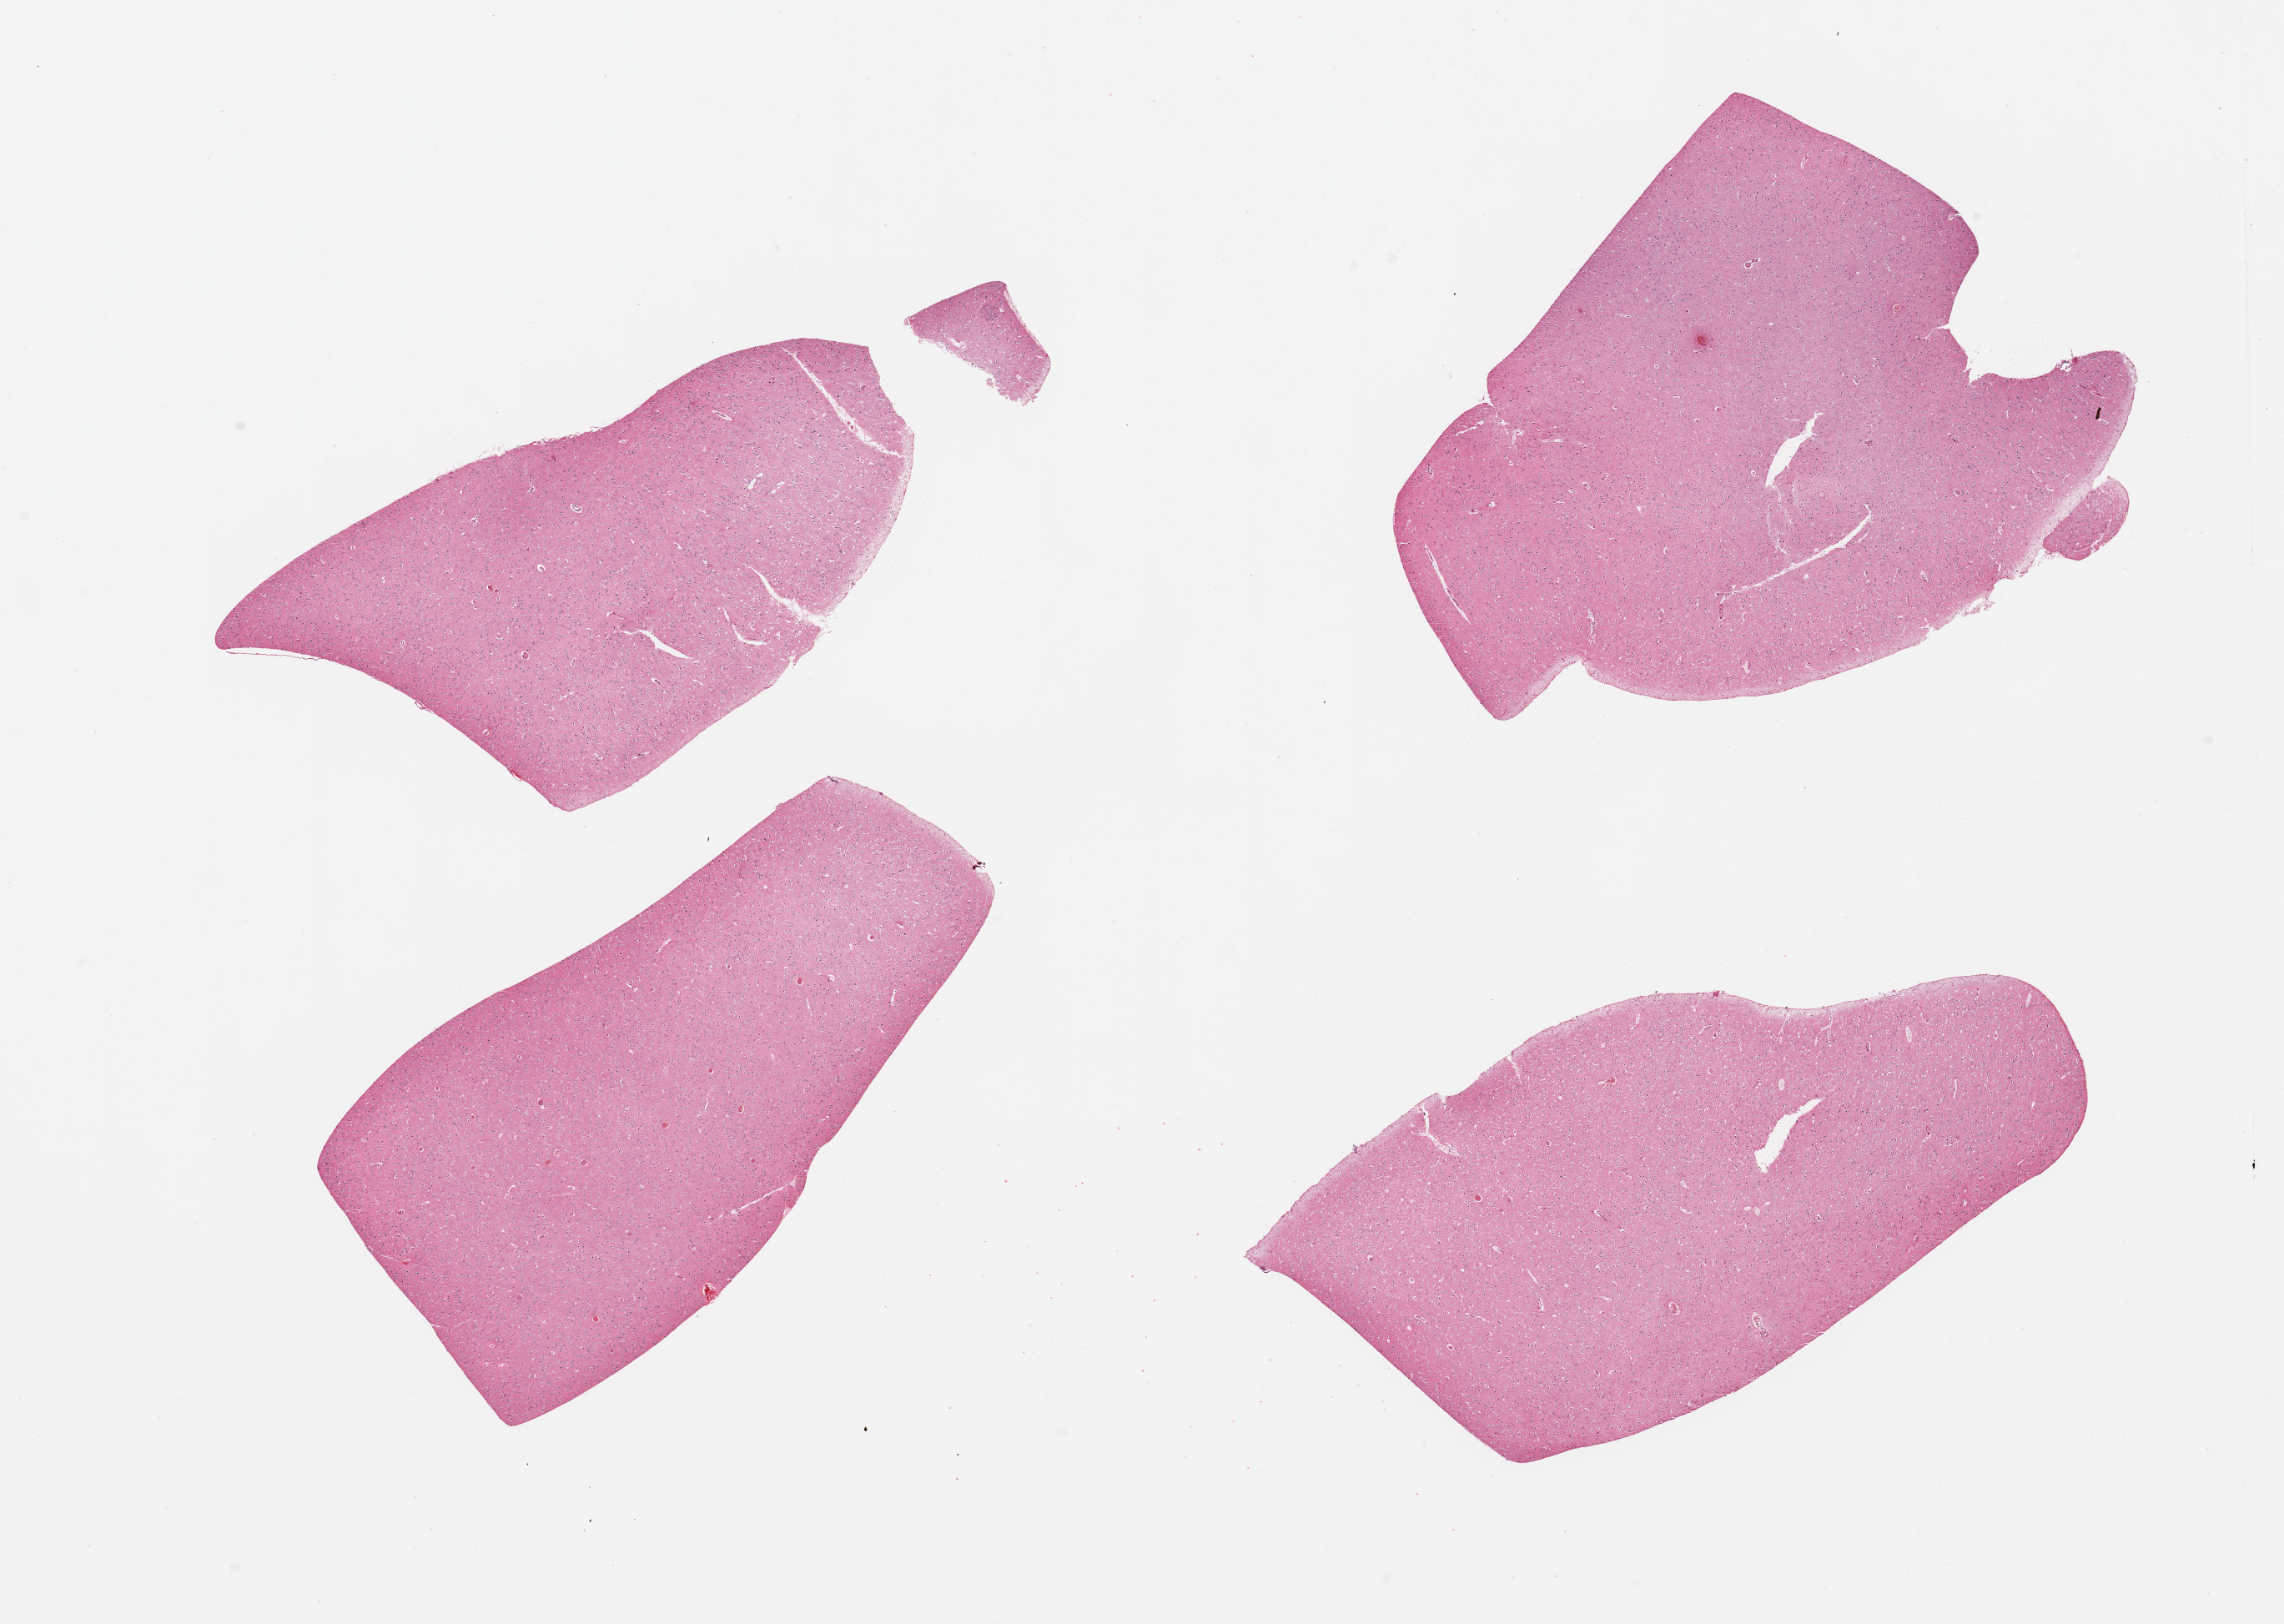
Hematoxylin and eosin (H&E) whole-slide image, brightfield, low-resolution overview of the scanned area, about 21.7 x 15.4 mm (slide scanned at 20x), PAXgene-fixed paraffin-embedded (PFPE) section, target tissue: cerebral cortex, donor tissue sample. Male donor.
Pathologist's review note for this sample: 4 pieces, no abnormalities.